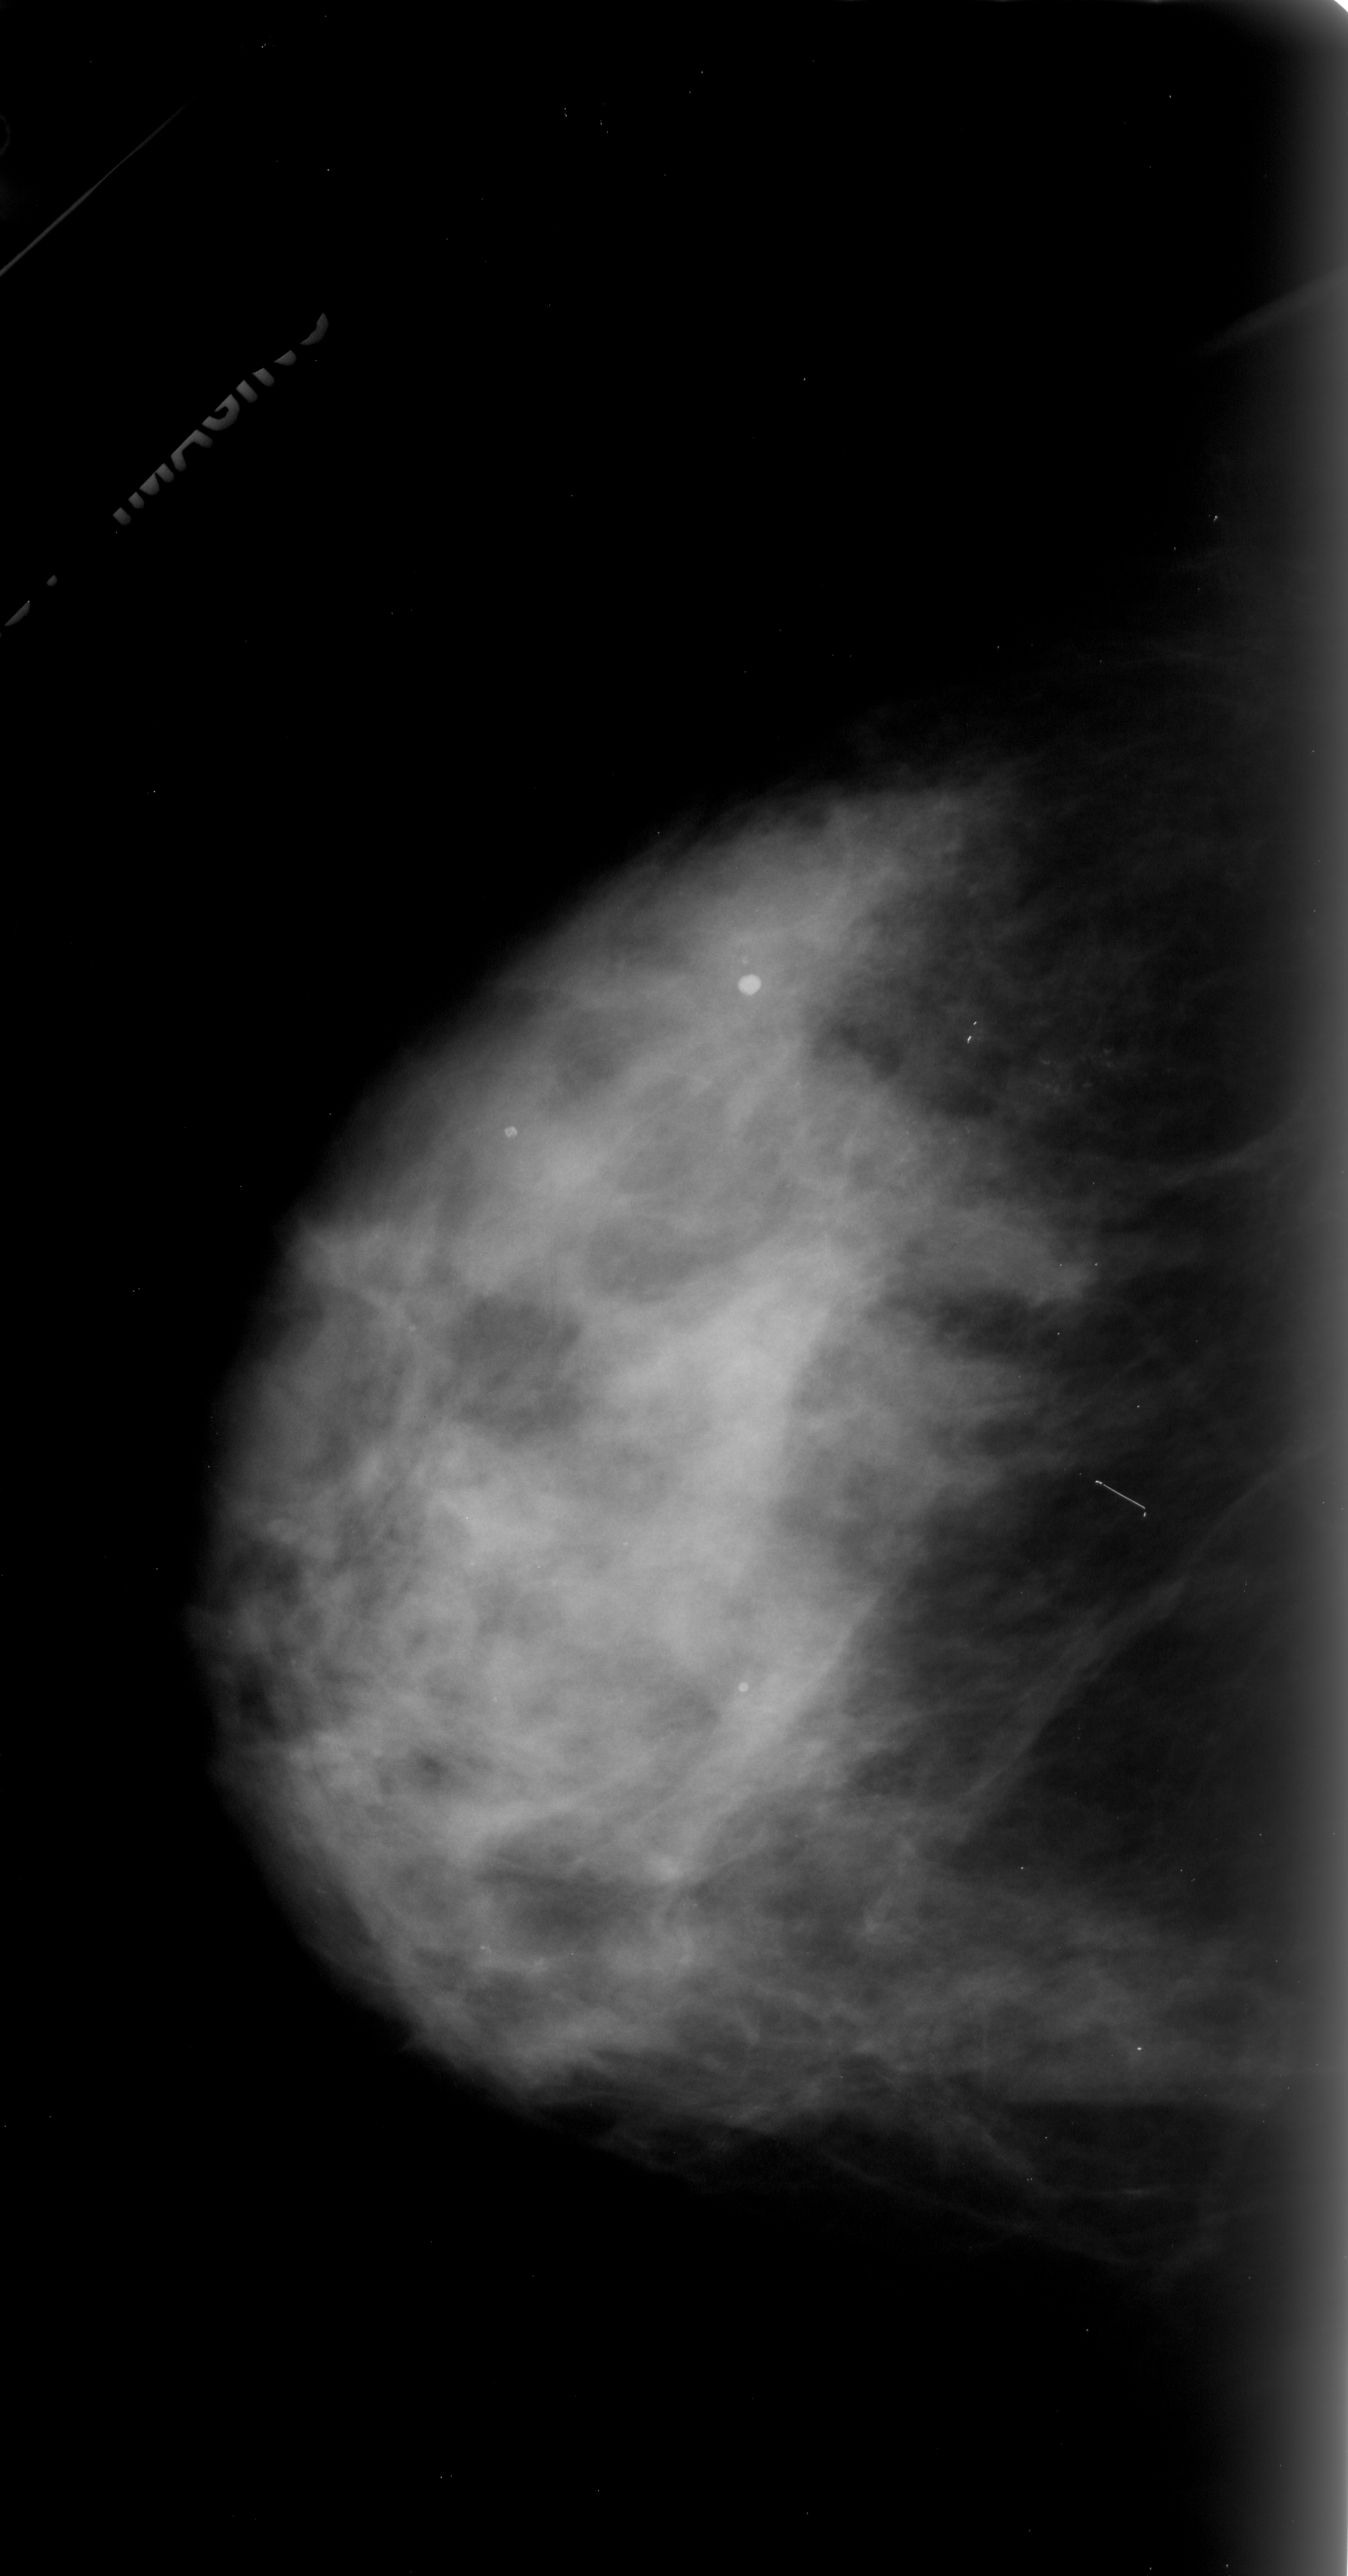
Scanned film-screen mammogram; left breast; CC view.
Marked findings (only marked abnormalities are described; nothing is implied about the rest of the image): calcifications, morphology pleomorphic, distribution linear; BI-RADS assessment category 4; subtlety rating 2 on a 1 (subtle) to 5 (obvious) scale; pathology result (as recorded, not read from the image): malignant.